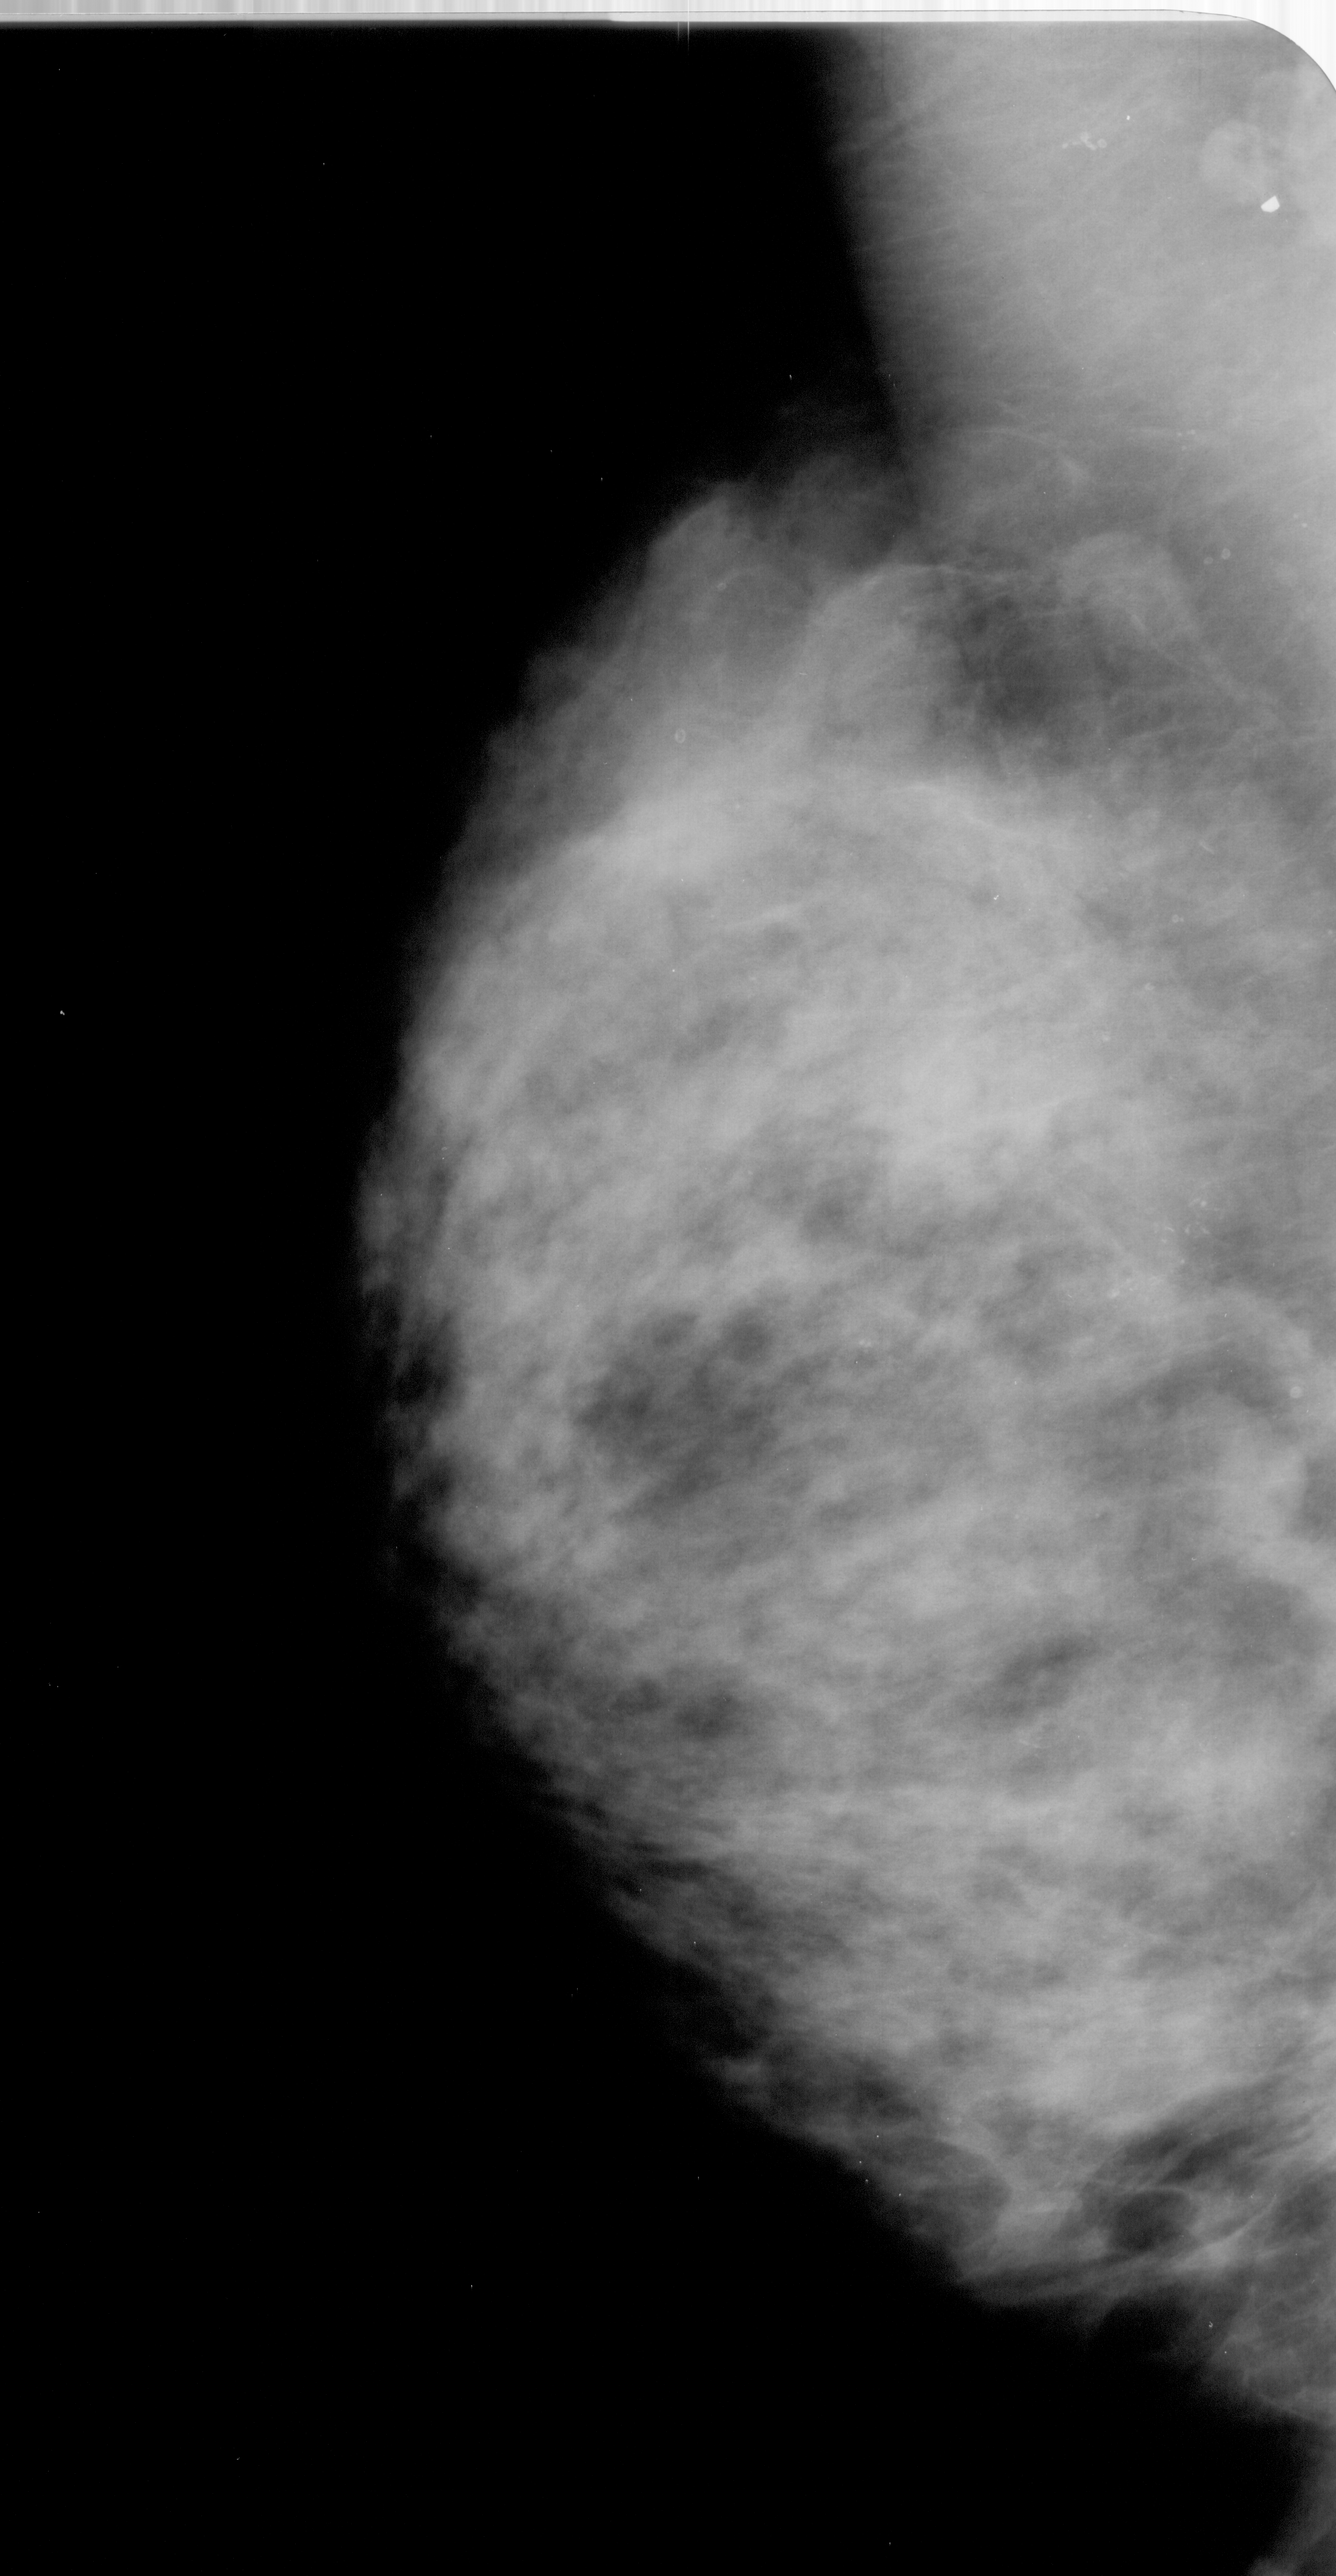
Scanned film-screen mammogram; left breast; MLO view; BI-RADS breast density category 3 (scale 1–4); 1336 × 2576 image matrix.
Expert-marked regions of interest on this image (one box per marked abnormality):
- calcifications, morphology pleomorphic, distribution clustered; BI-RADS assessment category 4; pathology (as recorded): malignant: bounding box <1124,1241,1255,1375> (left, top, right, bottom; pixels)